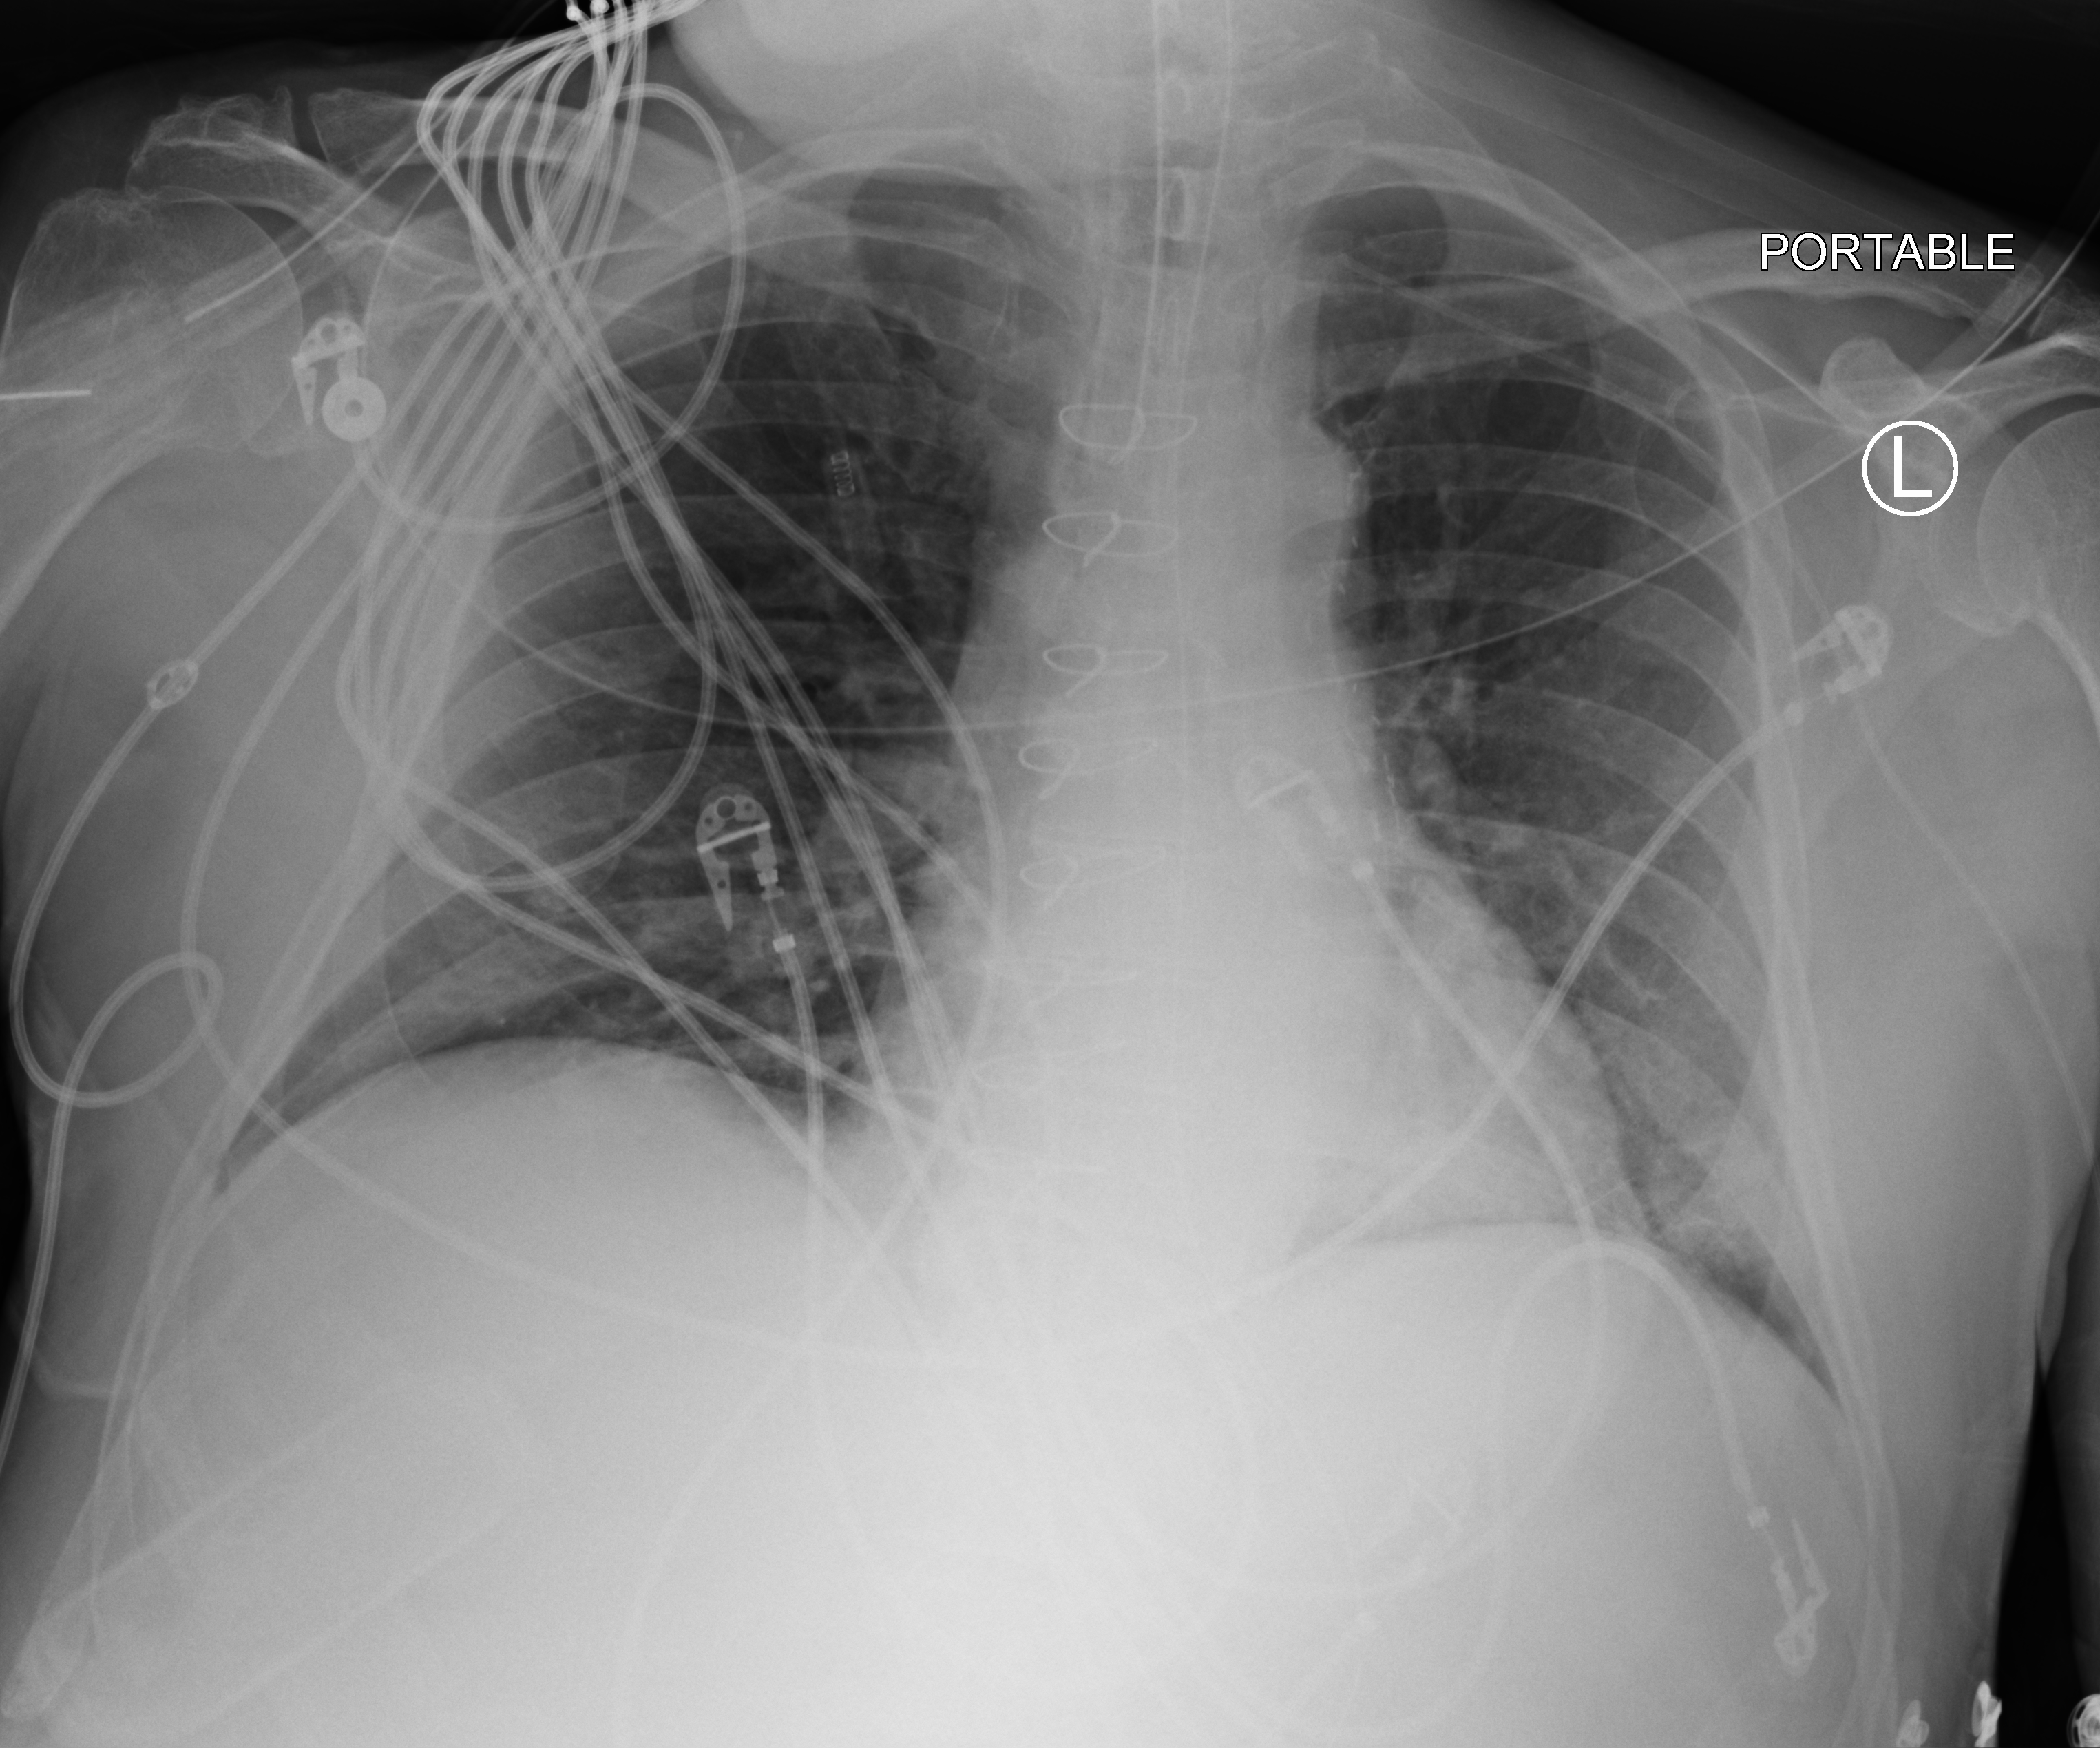
Bedside chest radiograph (computed radiography); anteroposterior (AP) projection. Male patient hospitalised with COVID-19, age 60–74 years.
From the hospital-stay record, not from the radiograph (when in the stay this image was taken is not recorded): smoking status (admission record): never; length of hospital stay: 22 days.